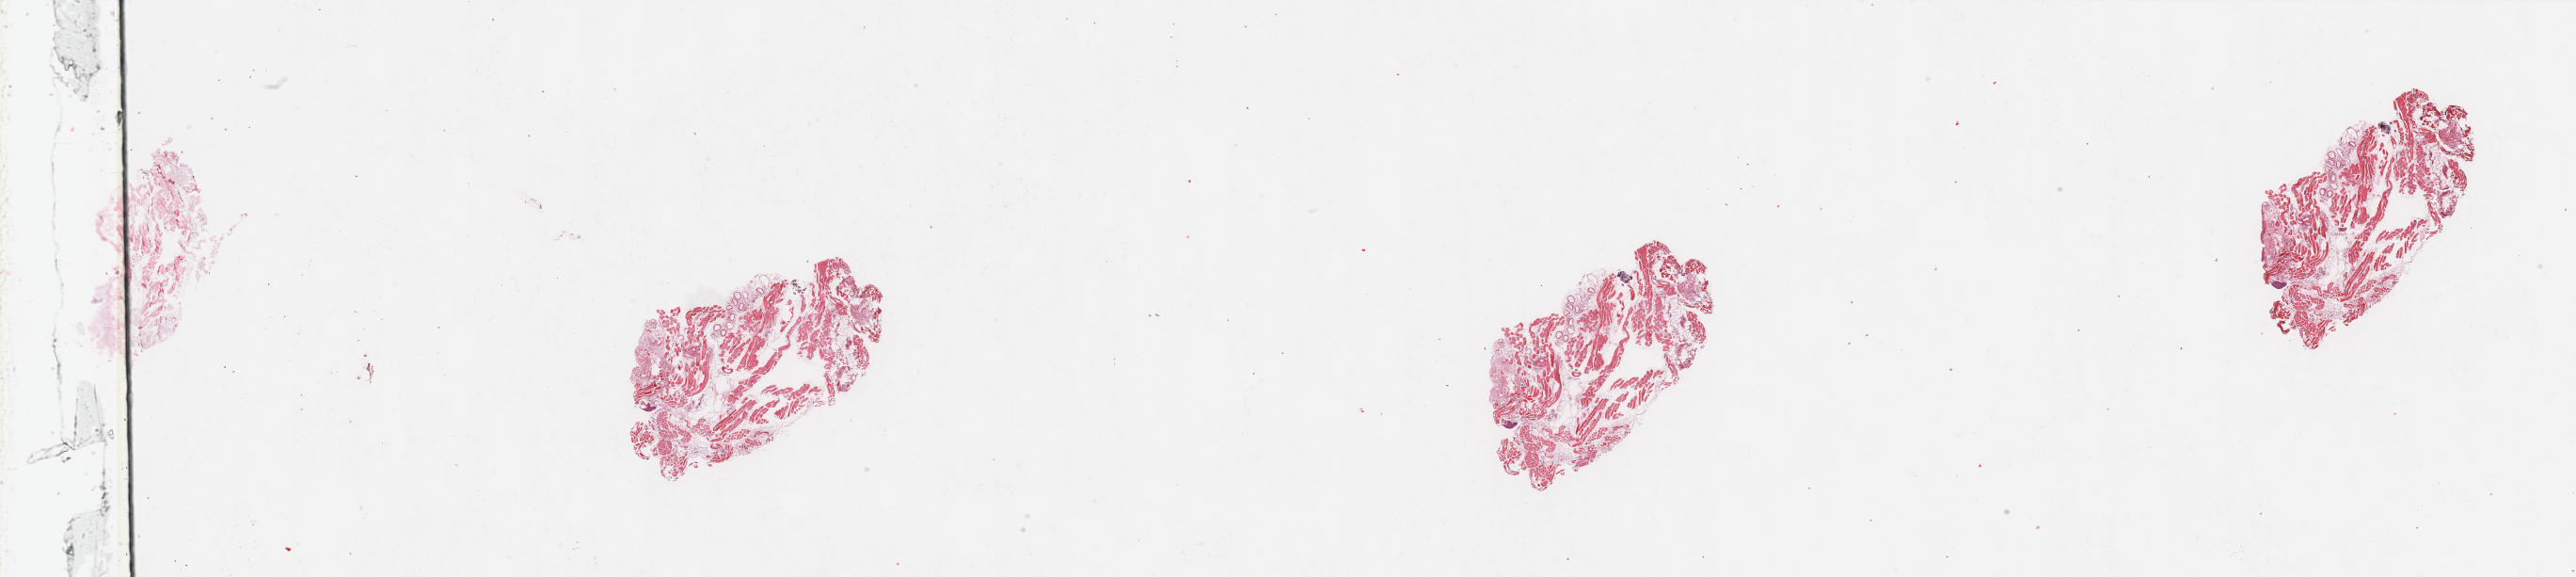
Whole-slide histology image, Hematoxylin and eosin (H&E) stained — whole scanned area (about 43.3 x 9.7 mm) shown as a low-resolution overview; head and neck, tissue type not recorded. 73-year-old male patient.
* patient diagnosis: Squamous cell carcinoma, NOS (oropharynx, NOS)